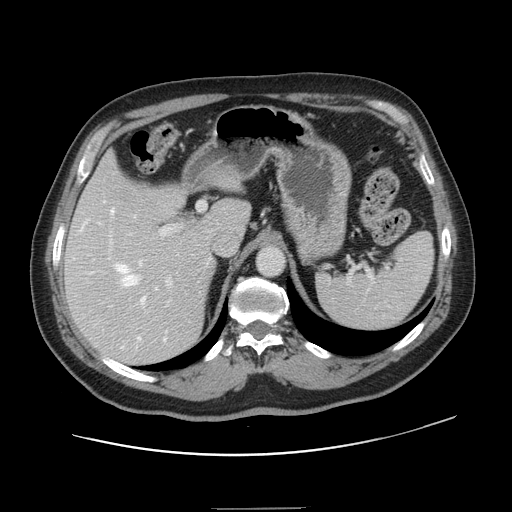
Contrast-enhanced abdominal CT, one axial slice; slice 96 of 143 in the series (ordered by position); 120 kVp; intravenous contrast given; soft-tissue window (W 400 / L 40 HU); 2.5 mm slice thickness; 512 × 512 image matrix, field of view 402 × 402 mm. Male patient, age 62 years. Case-level facts recorded for this patient, not image findings: diagnosis: colorectal cancer liver metastases, imaged before liver resection; multiple liver metastases: yes; largest metastasis: 2.7 cm; chemotherapy before resection: yes.
Structures marked on this image (expert manual segmentation):
- hepatic veins: bounding box (x1, y1, x2, y2) in pixels: (82, 201, 166, 348)
- liver: (66, 156, 249, 364)
- planned liver remnant (the part of the liver to remain after resection): (68, 156, 249, 256)
- portal vein (with intrahepatic branches): (74, 202, 205, 307)